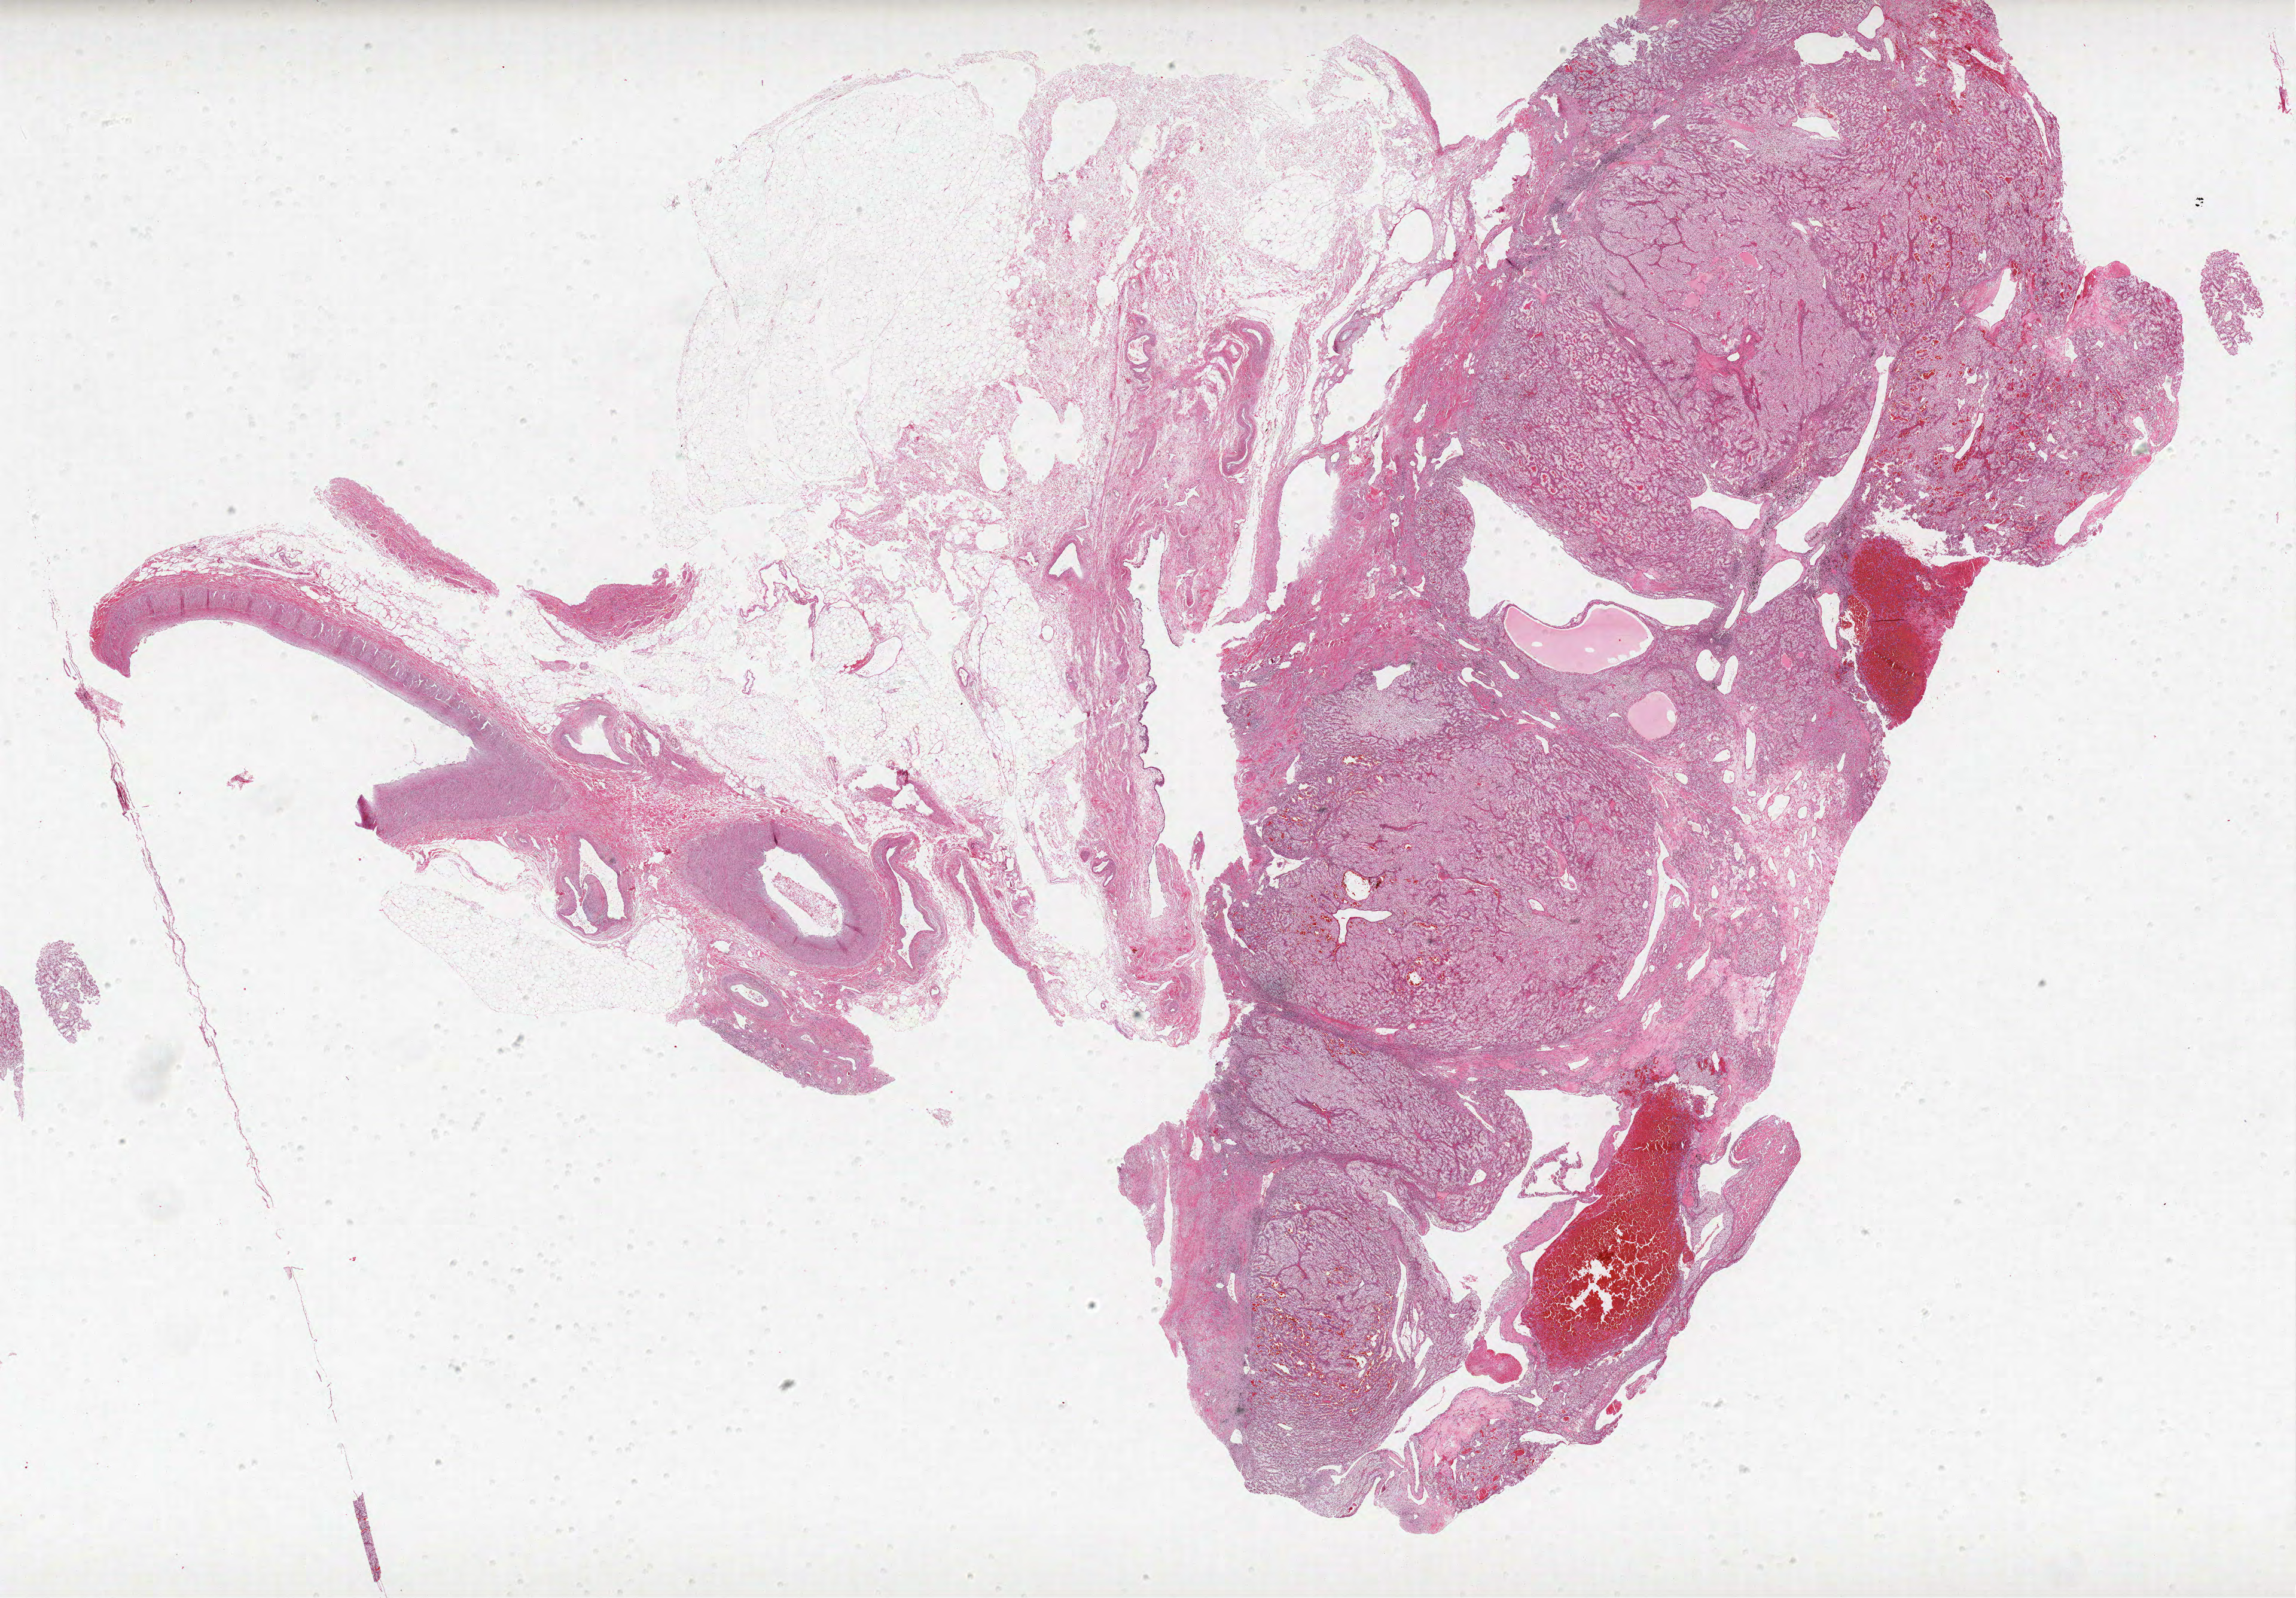
Digitized H&E-stained tissue section (whole slide) — low-resolution overview of the scanned area, about 30.7 x 21.4 mm (slide scanned at 40x). Formalin-fixed paraffin-embedded (FFPE) diagnostic section. Primary tumour sample from the kidney. Male, age 76 years at initial diagnosis. Histologic grade: G2 (moderately differentiated).
Lymph nodes positive (case pathology): 0 of 5 examined. AJCC pathologic stage: III. Diagnosis: Clear cell adenocarcinoma, NOS. TNM: T3a N0 M0. Laterality: right.